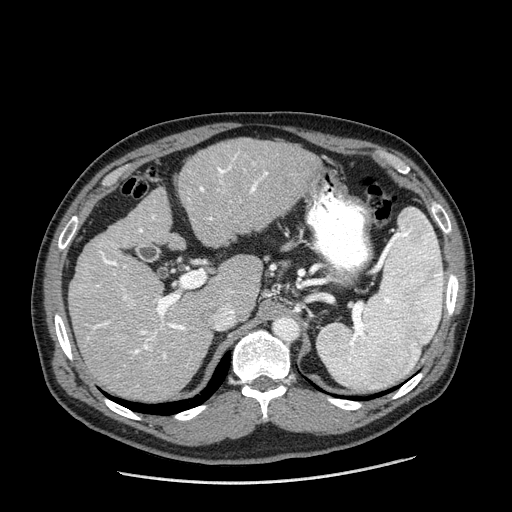
Contrast-enhanced abdominal CT (liver protocol), one axial slice; slice 117 of 198 in the series (ordered by position); 120 kVp; one of 2 acquisitions stored at this slice position; soft-tissue window (W 400 / L 40 HU); 512 × 512 image matrix, field of view 400 × 400 mm. From the clinical record (not read from this slice): diagnosis: hepatocellular carcinoma (patient treated with transarterial chemoembolisation; whether this scan precedes or follows treatment is not stated here); TNM stage (as recorded): Stage-II; Child-Pugh class: A; tumour size: 2.6 cm.
Structures marked on this image (semi-automatically segmented with operator editing):
- liver parenchyma outside the tumour (the mass and vessels are separate outlines, so this box may not span the whole liver): bounding box [x1, y1, x2, y2] px = [68, 138, 320, 400]
- liver vessels: [88, 154, 268, 359]